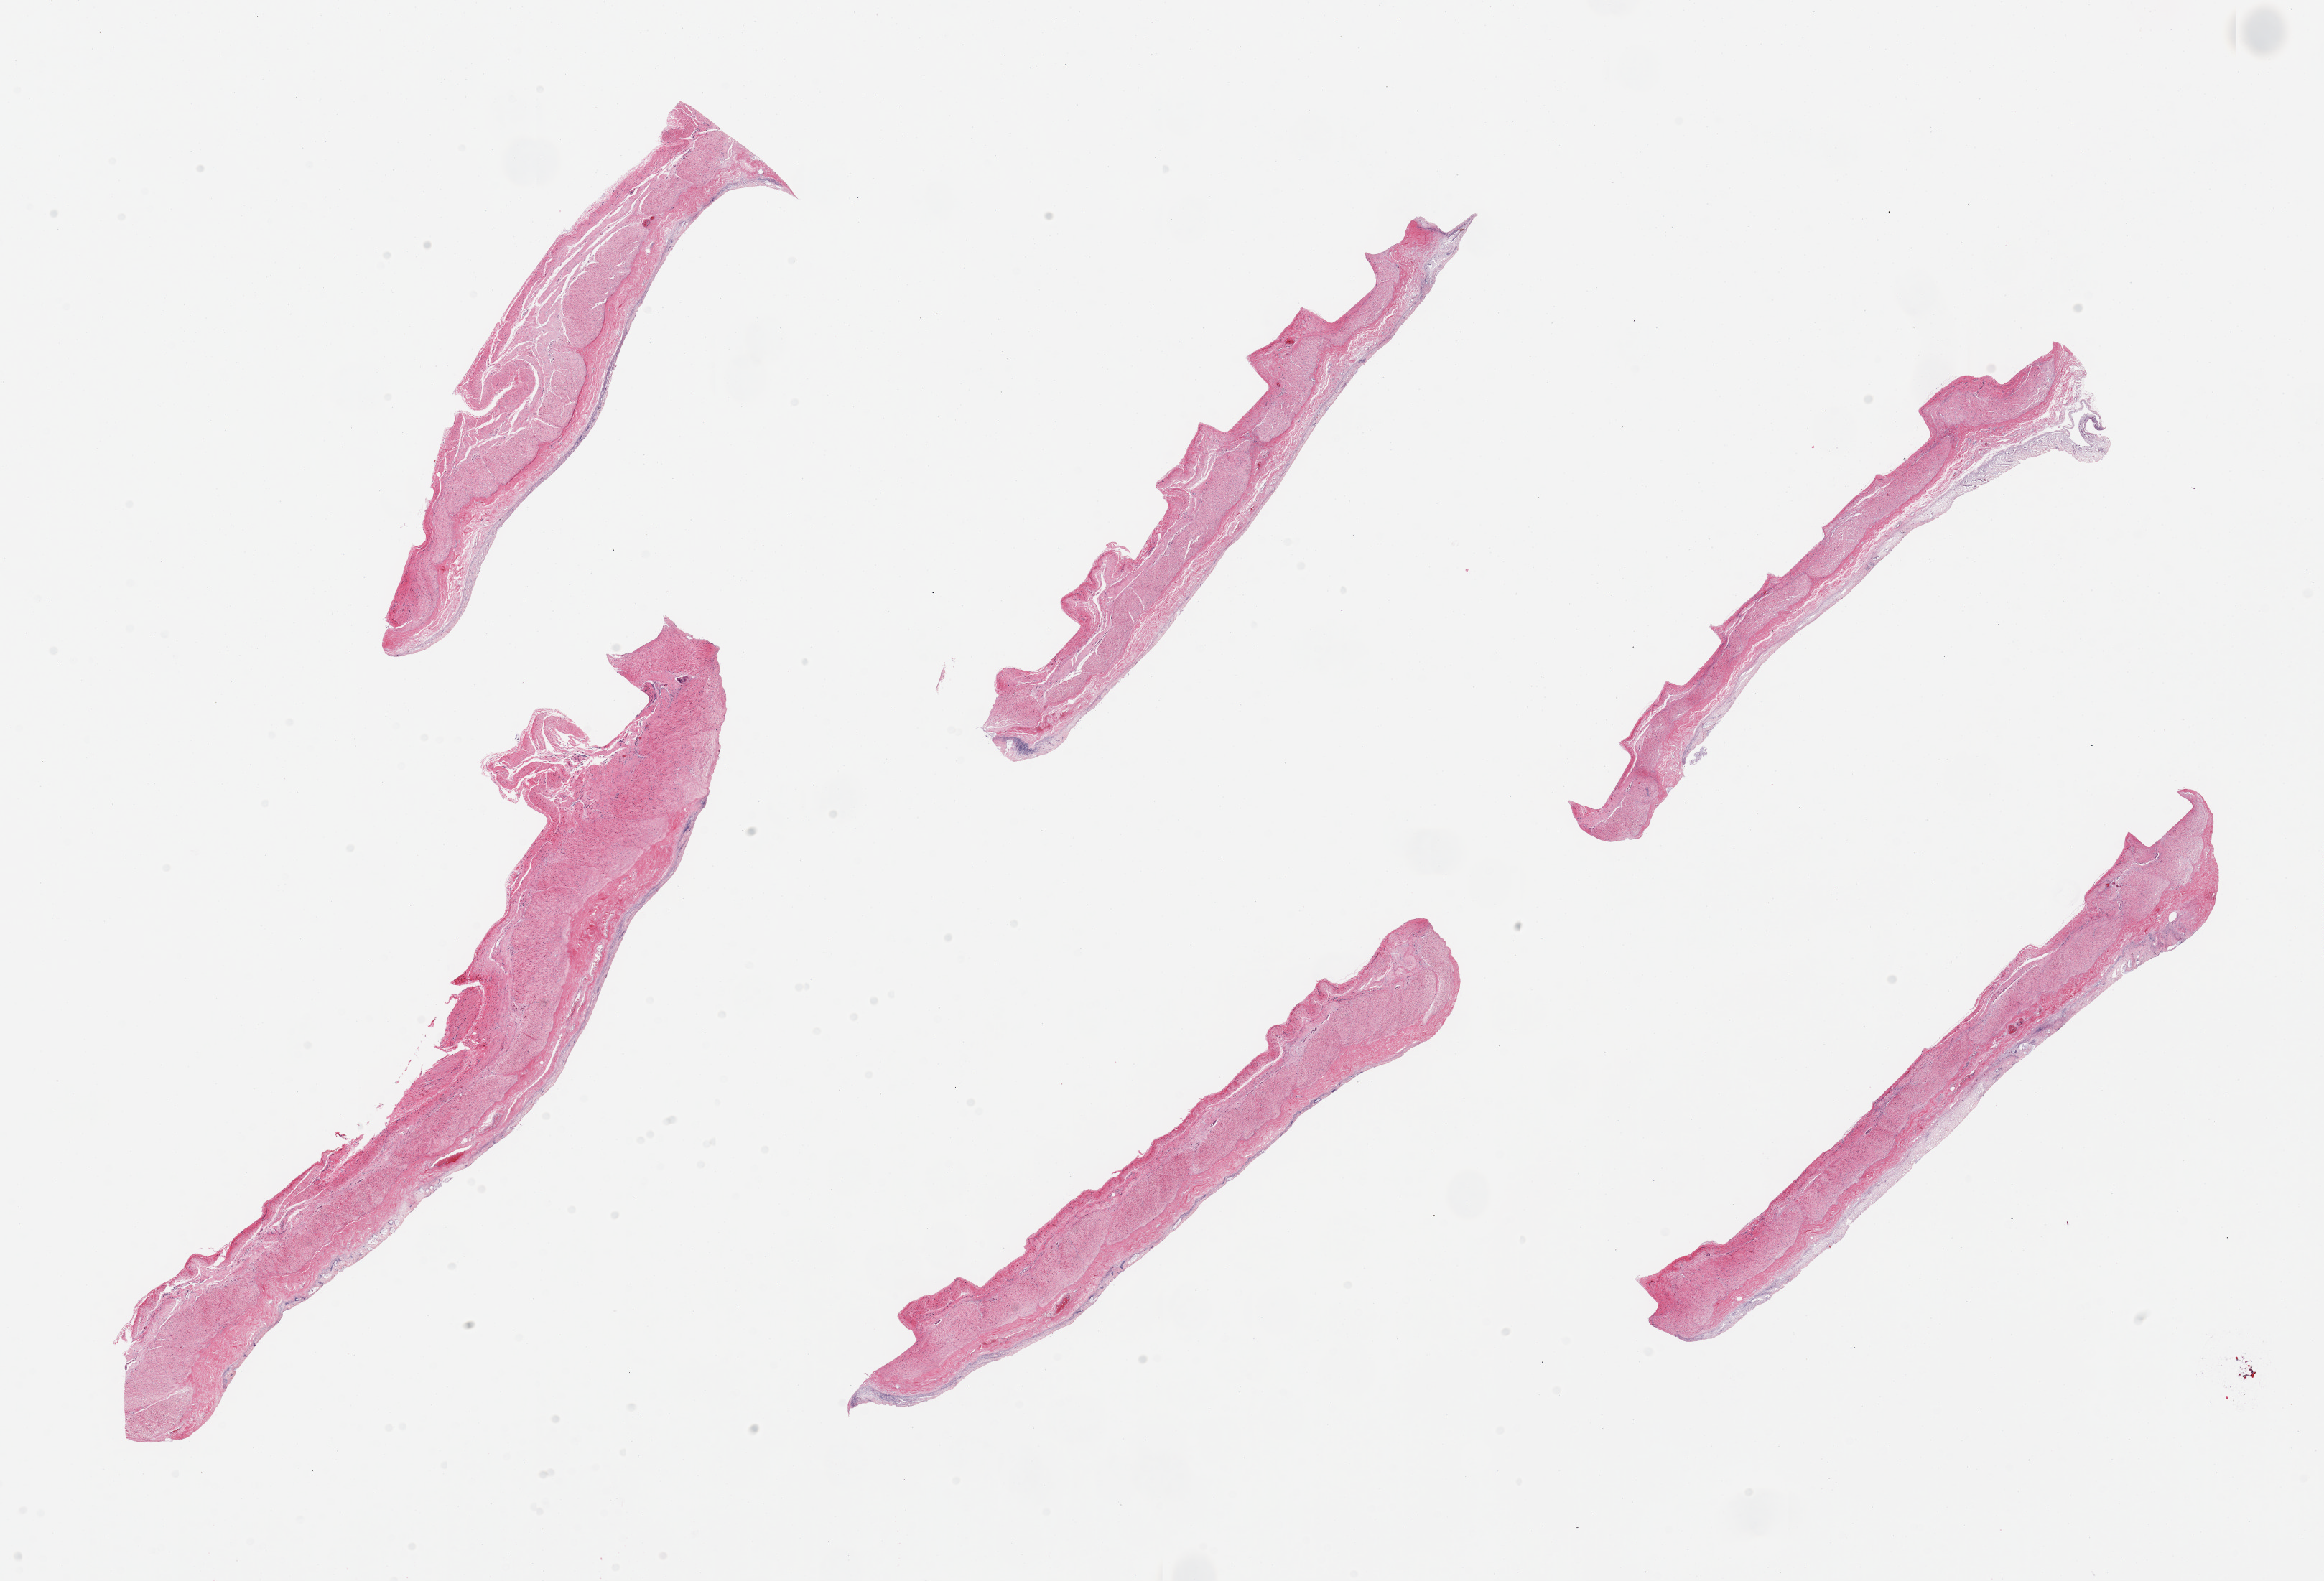
Hematoxylin and eosin (H&E) whole-slide image, low-resolution overview of the scanned area, about 25.6 x 17.4 mm (slide scanned at 20x); PAXgene-fixed paraffin-embedded (PFPE) section; sampled site (target tissue): transverse colon; tissue donor sample.
• pathologist's review note for this sample: 6 pieces, mucosa up to ~0.2mm but totally autolyzed